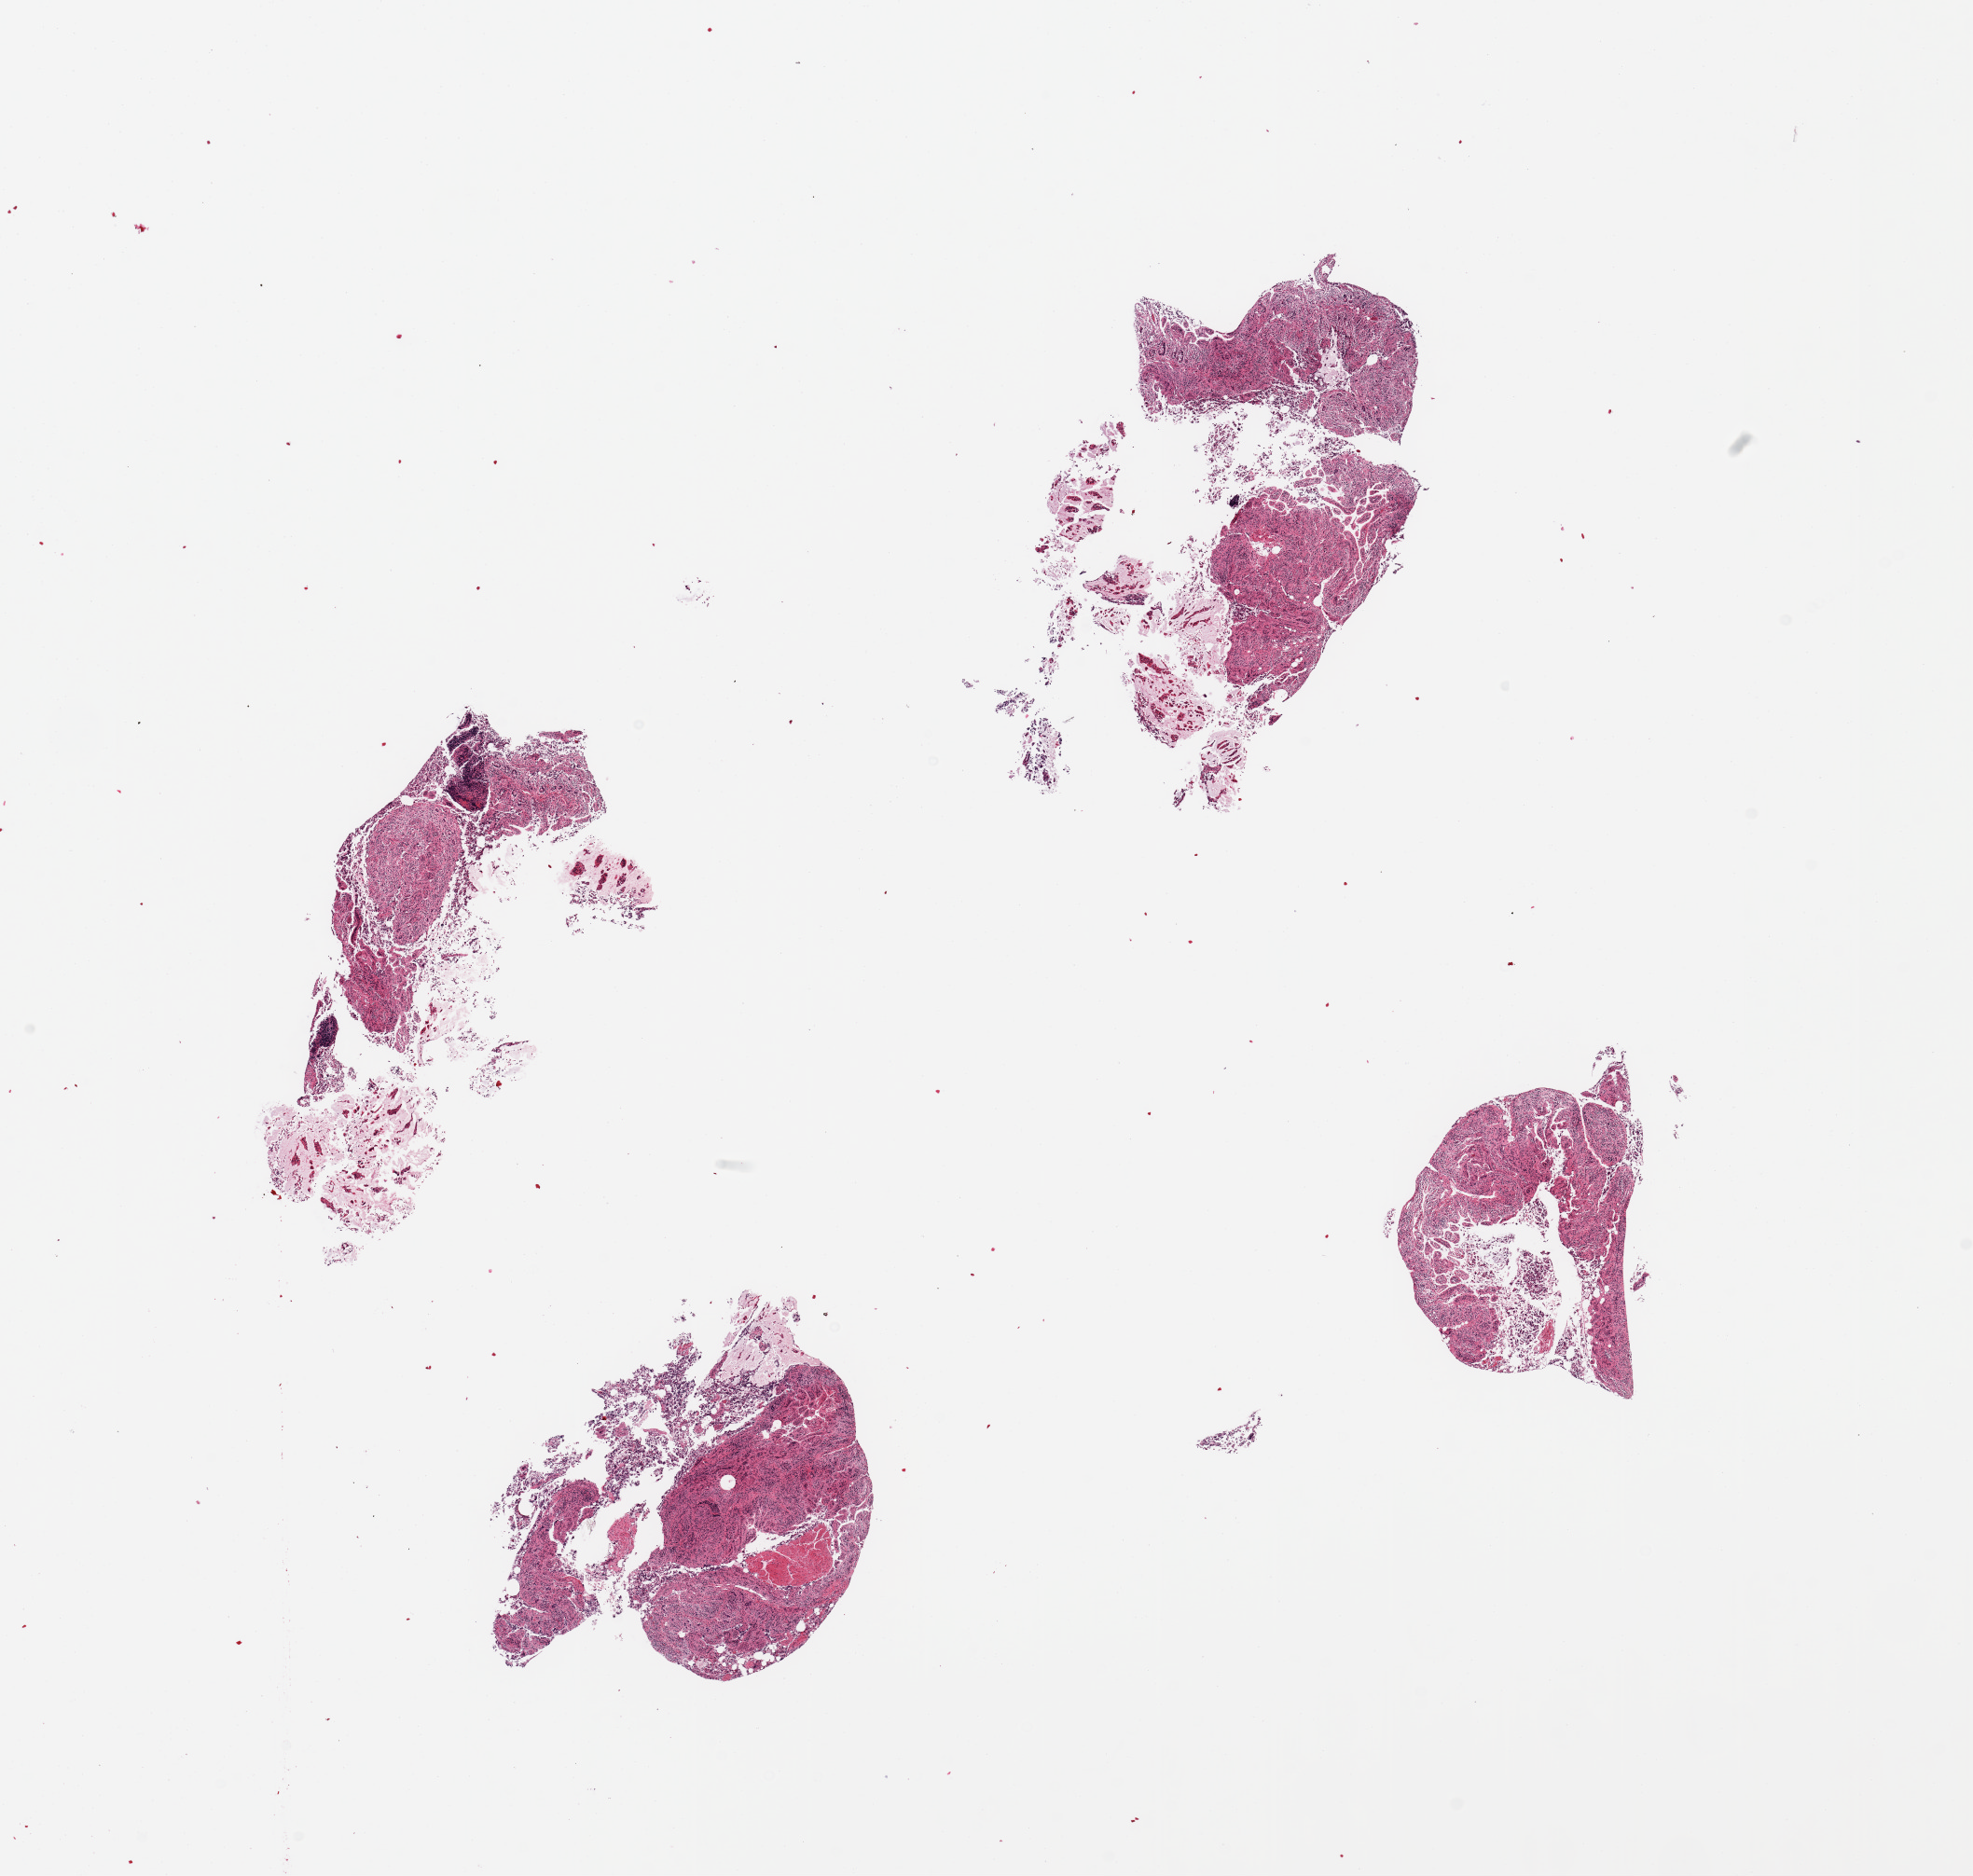
Whole-slide image, H&E stain — shown as a low-resolution overview of the whole scanned area (about 16.7 x 15.9 mm, acquisition: 20x scan), PAXgene-fixed paraffin-embedded (PFPE) section, sampled site (target tissue): ileum, tissue donor sample.
Review note (as recorded): 4 pieces, no target lymphoid aggregates.